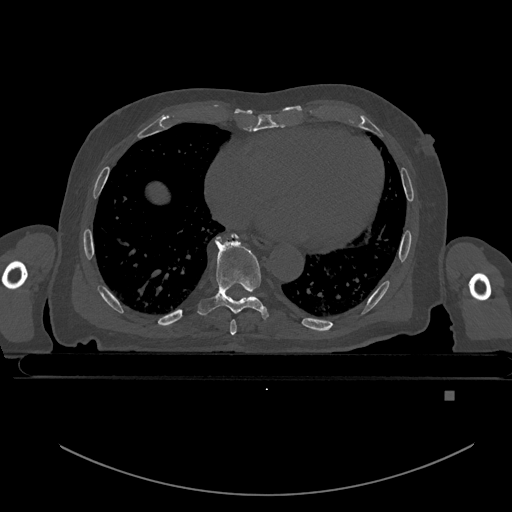
CT including the spine, one axial slice. Position 202 of 969 along the scan axis. Bone window (W 1800 / L 400 HU). 512 × 512 image matrix, field of view 456 × 456 mm. Male patient, age 82 years. From the clinical record (not read from this slice): primary cancer: prostate; vertebrae with lytic lesions (as recorded): T11, T9, T8, T2.
Outlined on this slice (semi-automatically segmented with operator editing):
- T7 vertebra: bounding box [x1, y1, x2, y2] px = [230, 320, 236, 335]
- T8 vertebra: [198, 234, 271, 320]
- T9 vertebra: [231, 235, 234, 238]